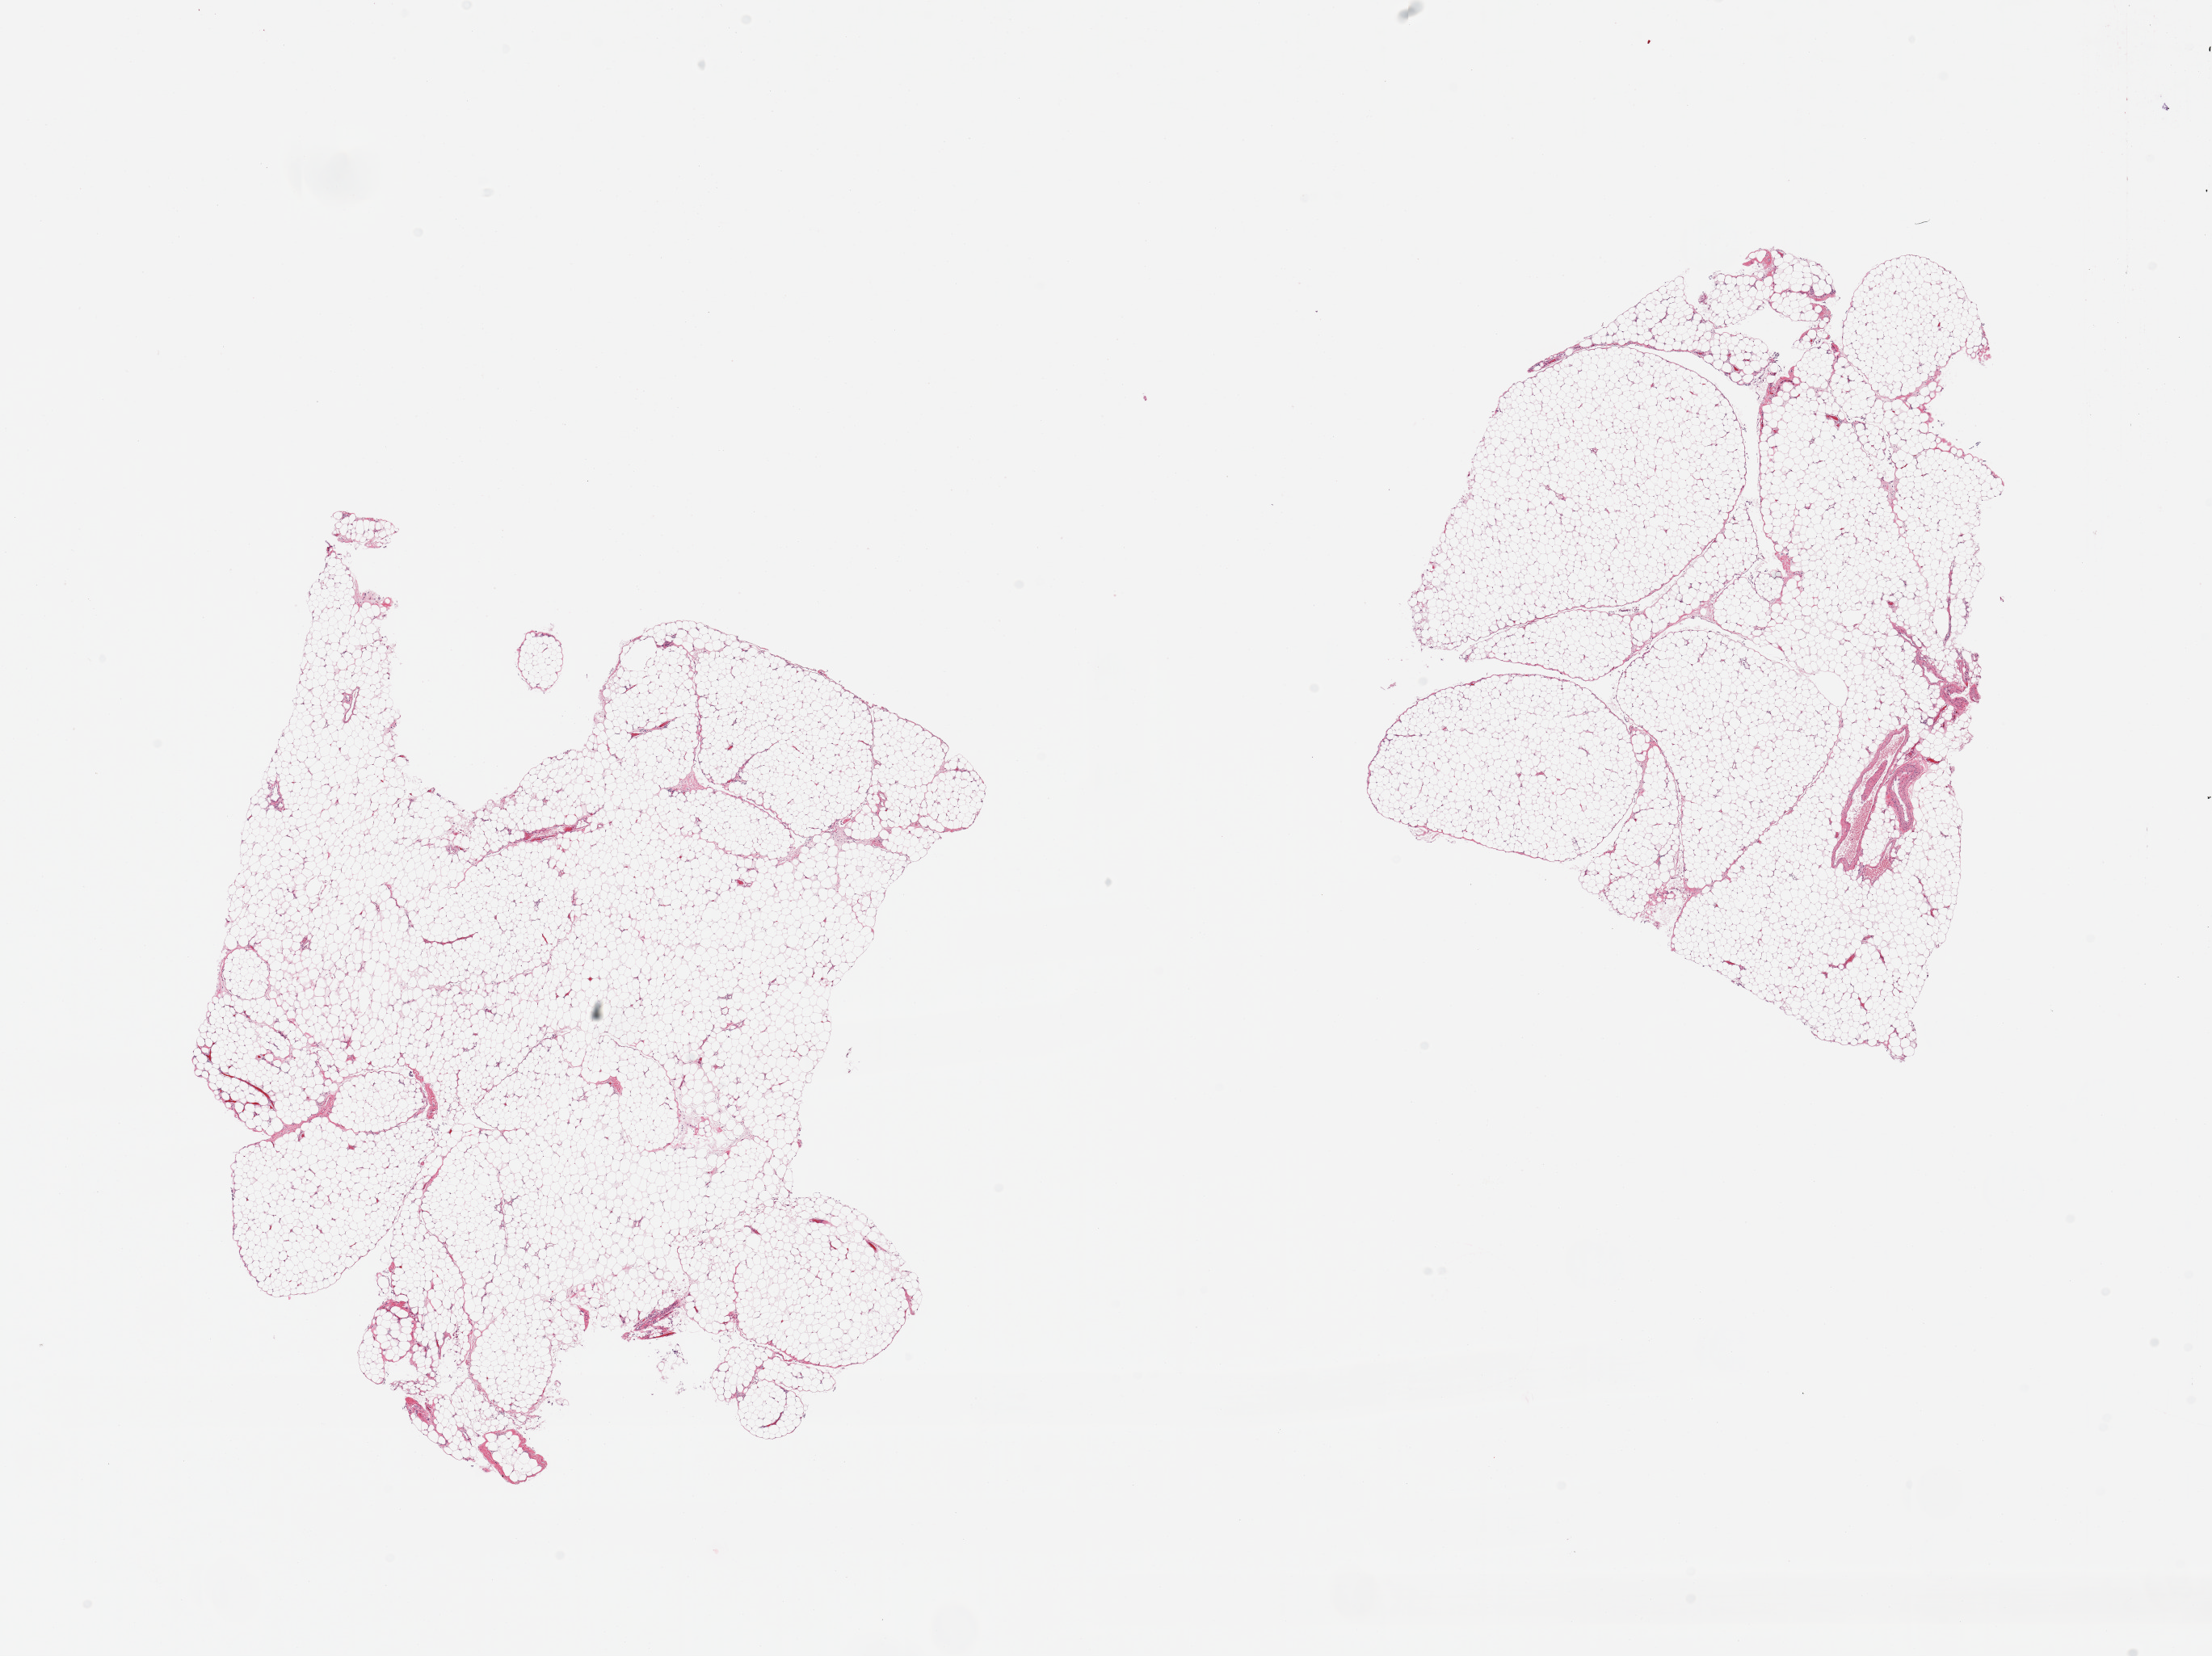
Whole-slide image, haematoxylin and eosin stain — shown as a low-resolution overview of the whole scanned area (about 21.7 x 16.2 mm, acquisition: 20x scan). PAXgene-fixed, paraffin-embedded tissue. Sampled site (target tissue): omentum. Tissue donor sample. Donor: male.
- review note (as recorded): 2 pieces; lobulated mature adipose tissue with minimal fibrovascular component